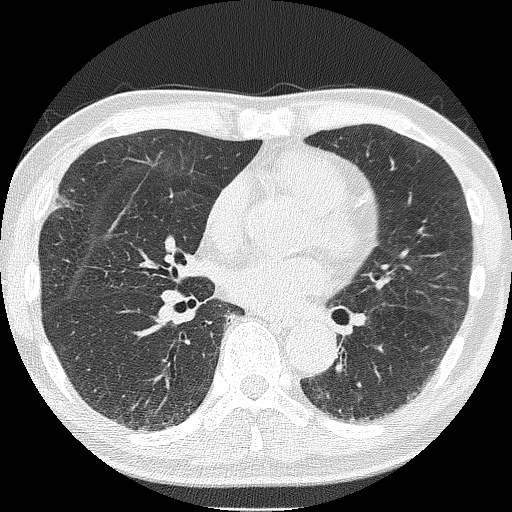
Low-dose screening chest CT, axial slice, second annual screen, lung window (W 1500 / L -600 HU), 2 mm slice thickness, lung (sharp) reconstruction kernel (FC51), slice 92 of 181 in the series, 512 × 512 image matrix. Male participant, aged 68 years at enrolment. Current smoker at enrolment.
Expert-annotated lung lesion, box from (x=34, y=182) to (x=85, y=227) px. Screening reader's record for this exam (one nodule recorded; not confirmed to be the boxed lesion): non-calcified nodule or mass ≥4 mm, right upper lobe, 6 × 4 mm, spiculated (stellate) margins, soft tissue attenuation, pre-existing on the prior screen: no. Official screen result: positive, other. Participant outcome: lung cancer diagnosed 22 days after this screen — squamous cell carcinoma, NOS, right upper lobe, moderately differentiated (G2), stage IA (AJCC 6th edition), 10 mm at pathology.